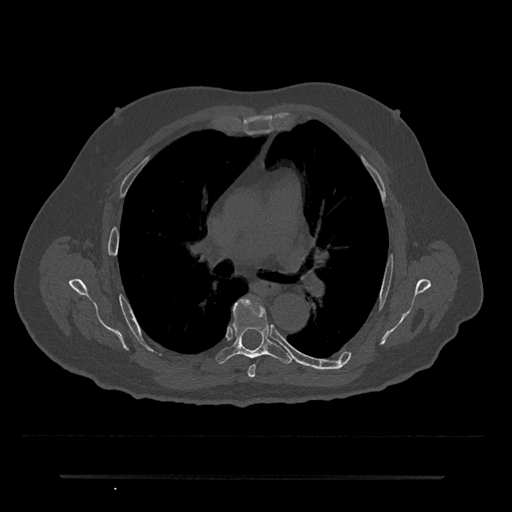
CT including the spine, one axial slice; position 446 of 797 along the scan axis; 120 kVp; bone window (W 1800 / L 400 HU); 512 × 512 image matrix, field of view 437 × 437 mm. Male patient, age 69 years. From the clinical record (not read from this slice): primary cancer: prostate.
Outlined on this slice (semi-automatic segmentation, software-assisted and operator-edited):
- T5 vertebra: box from (x=248, y=365) to (x=256, y=378) px
- T6 vertebra: (x=215, y=298)–(x=293, y=364)